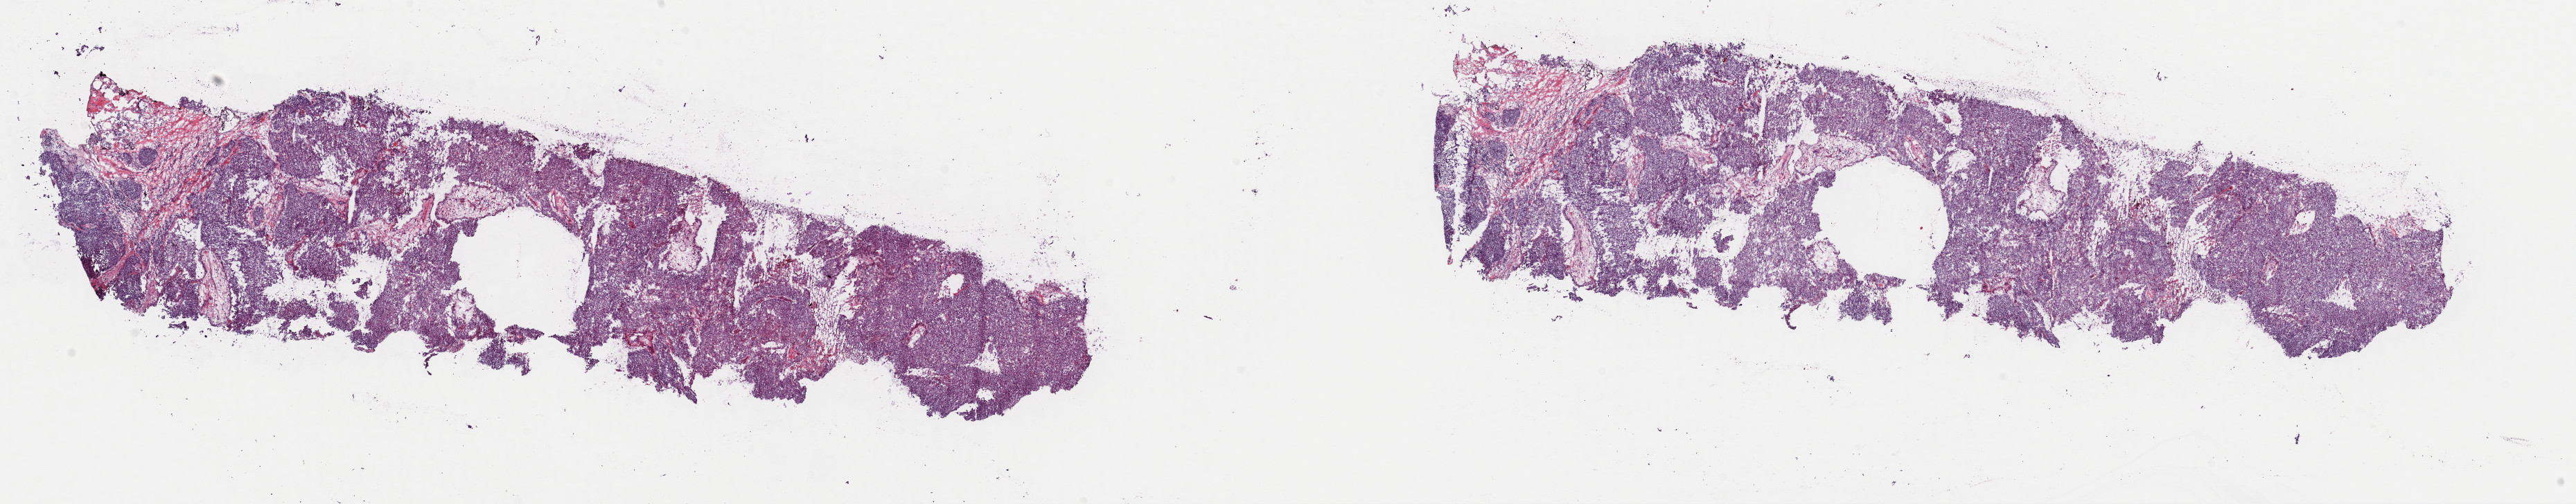
Whole-slide histology image, Hematoxylin and eosin (H&E) stained, a low-resolution overview of the entire scanned area, about 29.4 x 5.8 mm (slide scanned at 40x), frozen section from the top of the tissue portion, primary tumour sample from the breast. Female patient; age at initial diagnosis 72 years. Composition of this section per pathologist review: tumour cells 80%, tumour nuclei 80%, normal cells 0%, stromal cells 20%, necrosis 0%. Inflammatory infiltration, as recorded: lymphocyte infiltration 40%, monocyte infiltration 20%, neutrophil infiltration 20%.
Laterality: left. Lymph nodes positive (case pathology): 0 of 10 examined. Histologic diagnosis: Infiltrating duct carcinoma, NOS. AJCC pathologic stage: IIA.